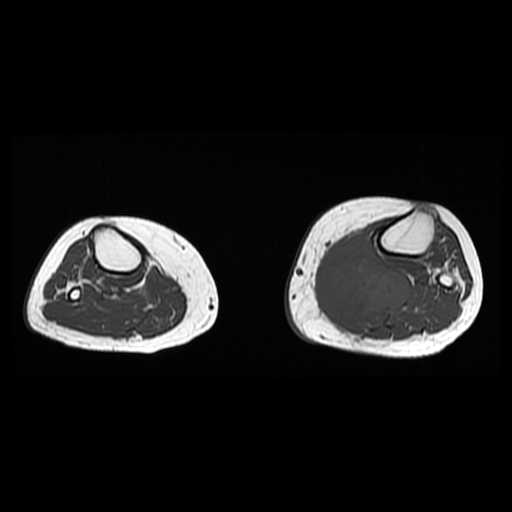
MRI of an extremity soft-tissue mass, one axial slice. Slice 20 of 38 in the series (ordered by position). 512 × 512 image matrix, field of view 330 × 330 mm. Female patient. From the clinical record (not read from this slice): histological type: extraskeletal high grade osteogenic sarcoma; grade: high; site of the primary tumour: left calf.
Annotated regions visible in this slice (outlined manually by an expert reader):
- gross tumour volume (mass): box from (x=314, y=232) to (x=413, y=325) px